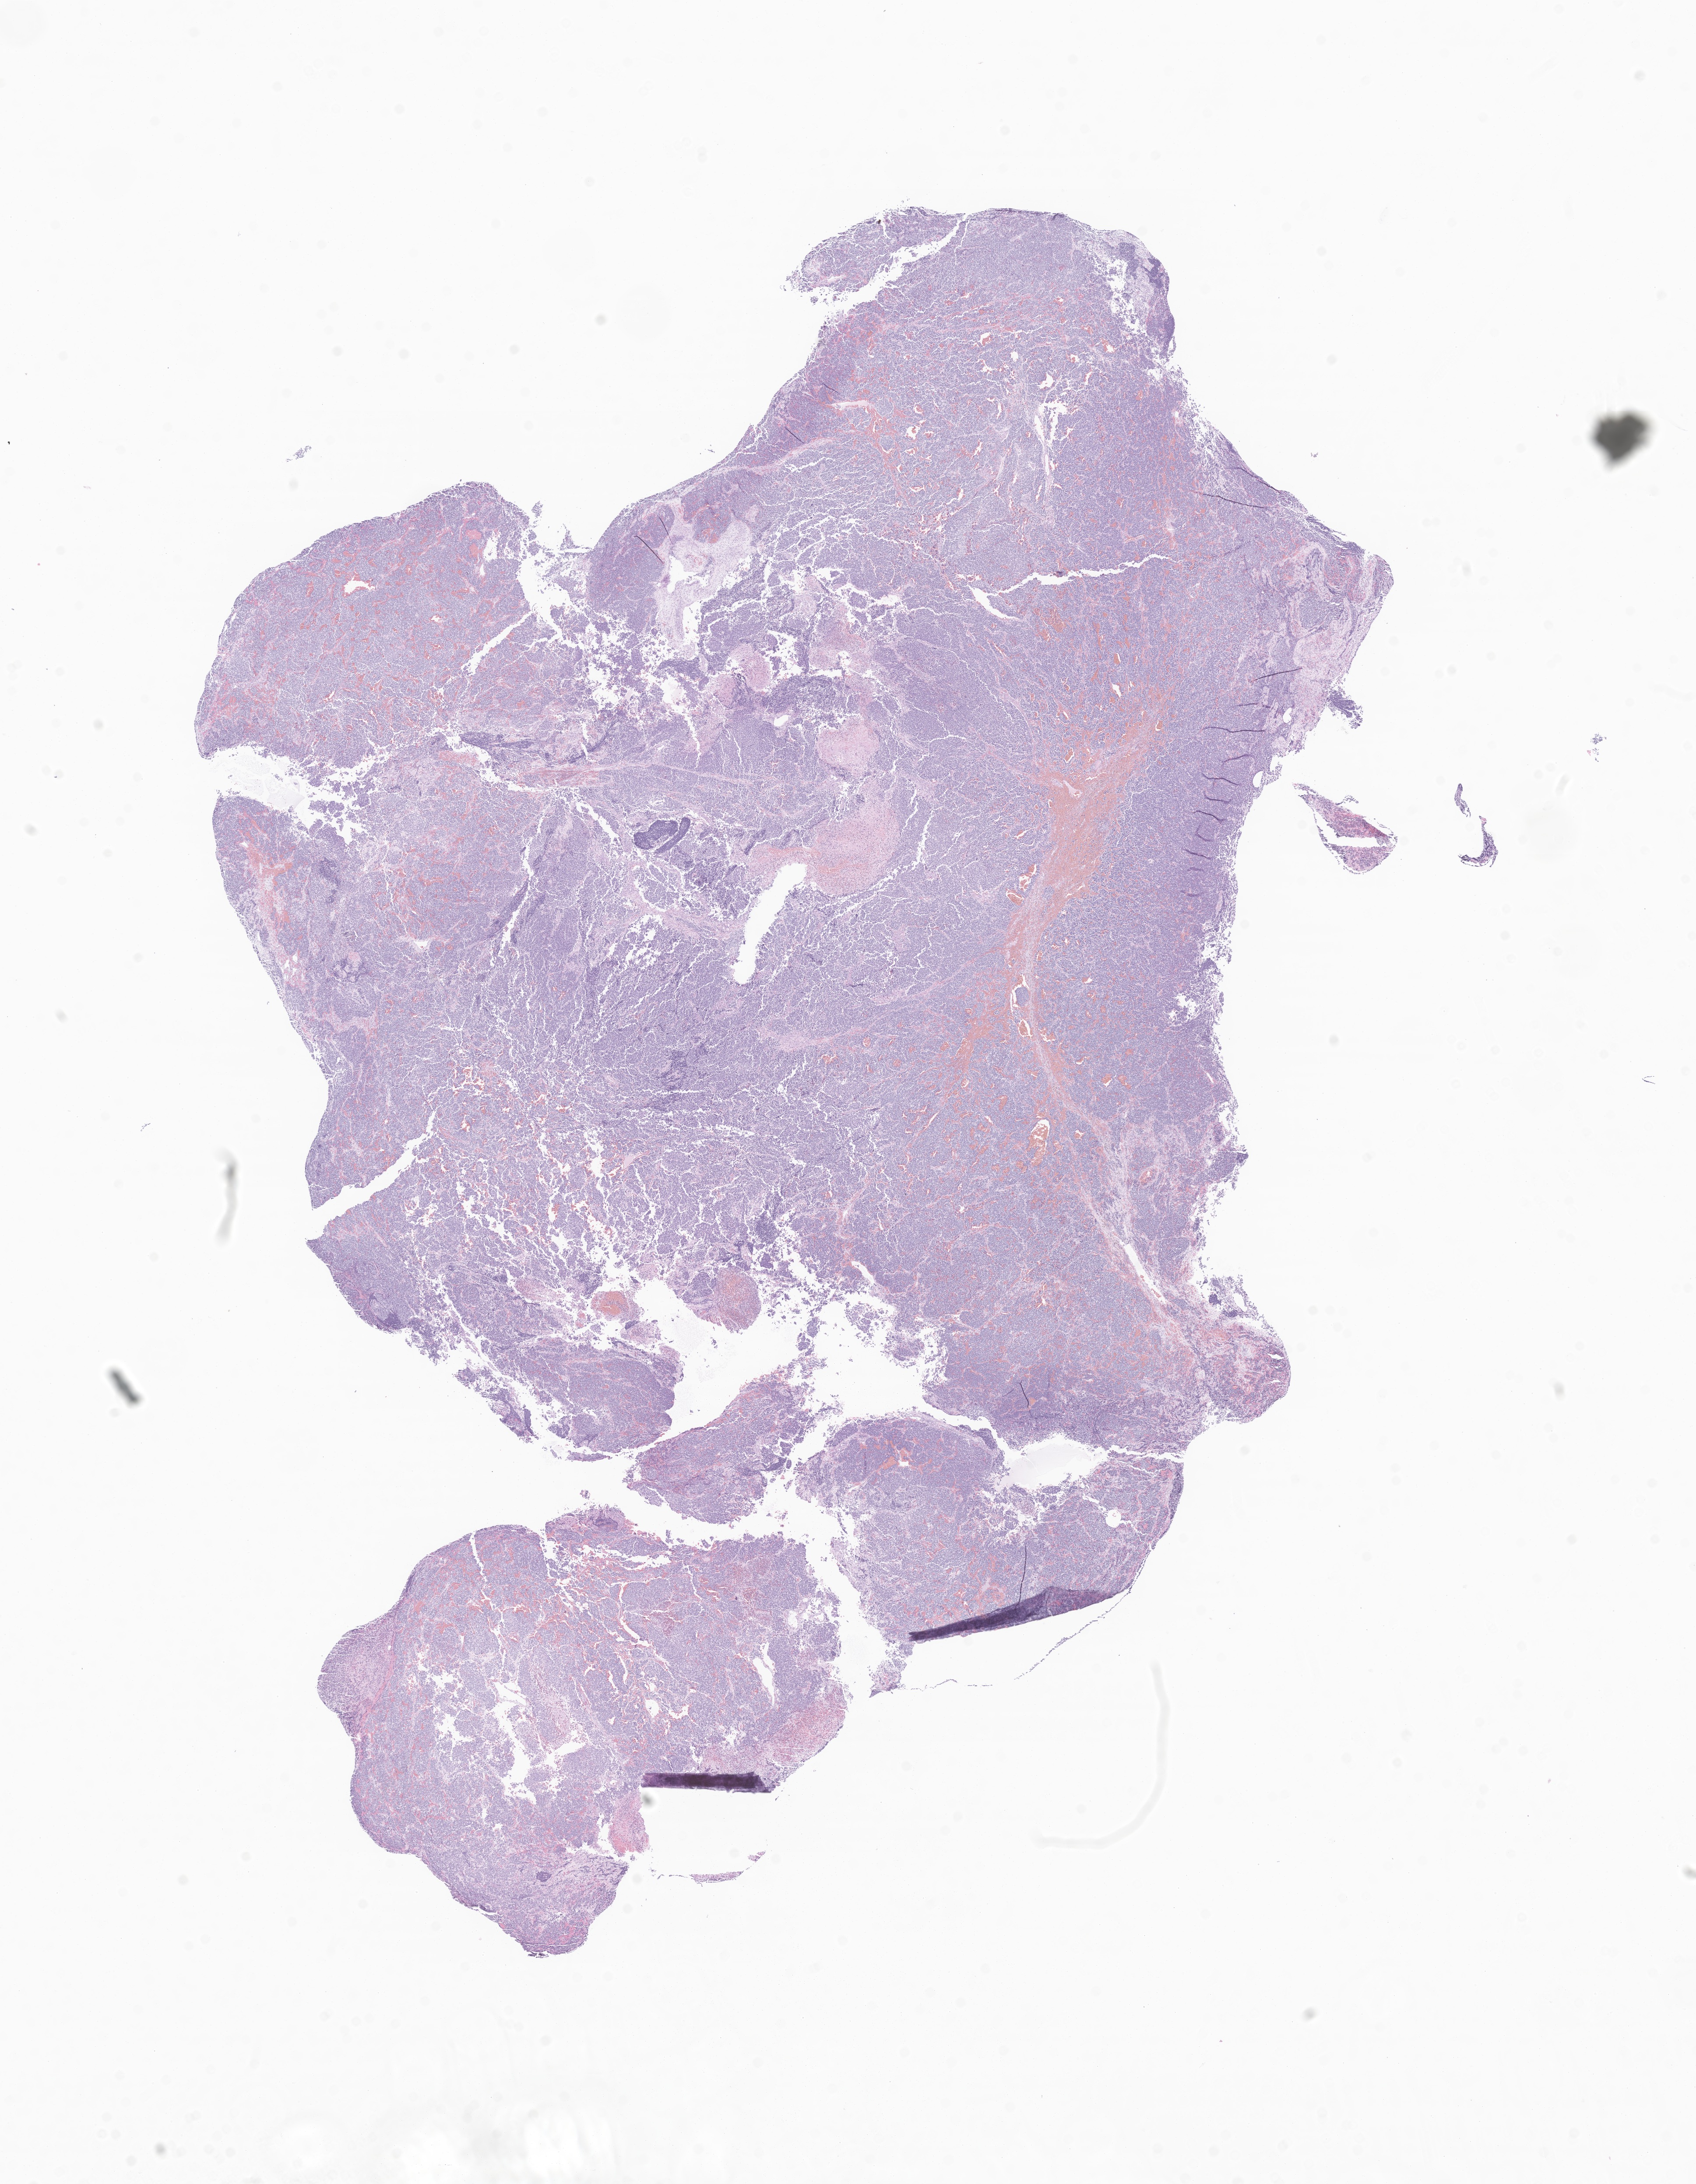
Whole-slide image, H&E stain of tumor tissue from the adrenal gland, low-resolution overview of the scanned area, about 16.3 x 21.0 mm. Formalin-fixed paraffin-embedded section. Male patient, age 786 days (about 2.2 years).
Diagnosis (ICD-O-3 morphology term): Neuroblastoma, NOS.